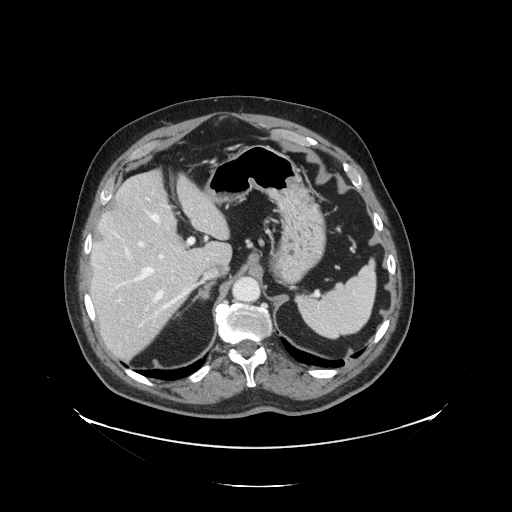
Contrast-enhanced abdominal CT, one axial slice; position 94 of 138 along the scan axis; intravenous contrast given; soft-tissue window (W 400 / L 40 HU); 2.5 mm slice thickness; 512 × 512 image matrix. Male patient, age 77 years. From the clinical record (not read from this slice): diagnosis: colorectal cancer liver metastases, imaged before liver resection; multiple liver metastases: no.
Structures marked on this image (expert manual segmentation):
- hepatic veins: box from (x=126, y=213) to (x=188, y=326) px
- liver: (x=91, y=172)–(x=231, y=360)
- planned liver remnant (the part of the liver to remain after resection): (x=92, y=172)–(x=230, y=288)
- portal vein (with intrahepatic branches): (x=116, y=238)–(x=194, y=303)